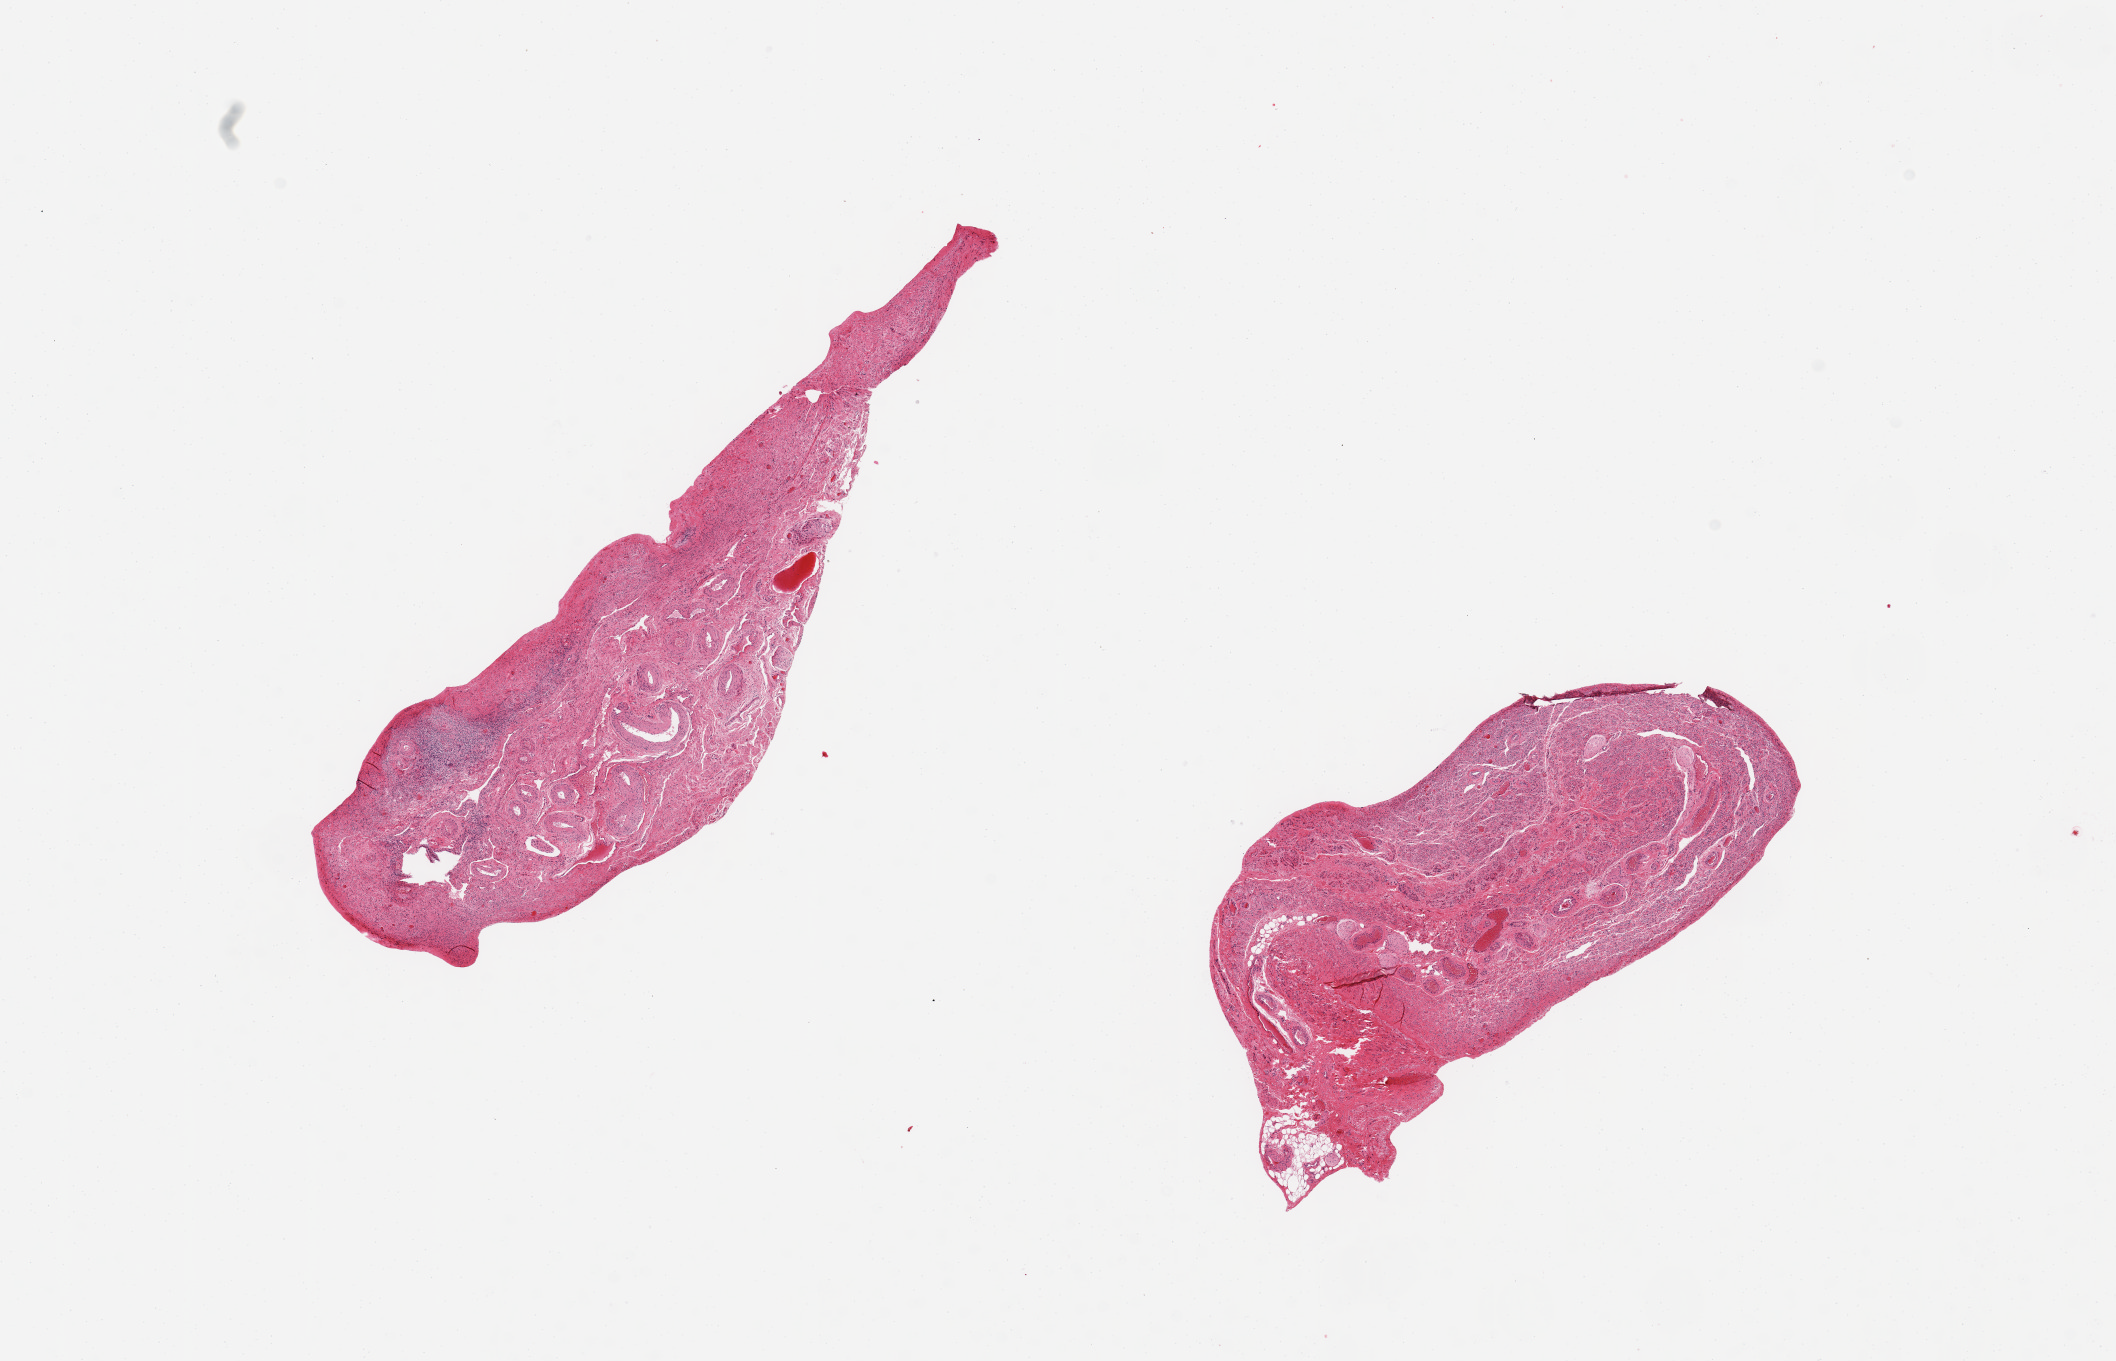
Whole-slide image, H&E stain, brightfield, a low-resolution overview of the entire scanned area, about 16.7 x 10.8 mm (acquisition: 20x scan). PAXgene-fixed, paraffin-embedded tissue. Section of fallopian tube (target tissue). Donor tissue sample. Donor: female.
• reviewer comment on this tissue sample: 2 pieces, 7x2 & 5x2 mm; no mucosa